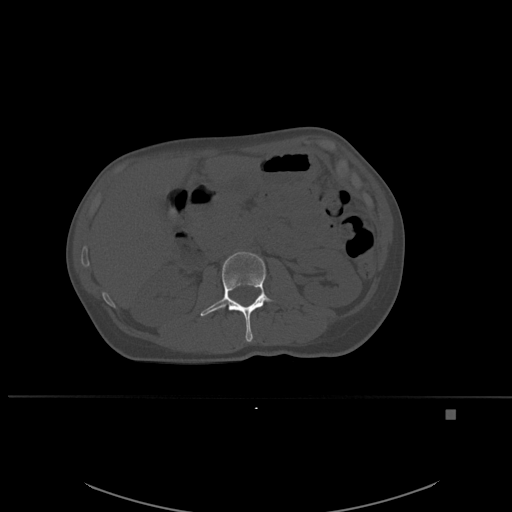
CT including the spine, one axial slice. Position 236 of 537 along the scan axis. Bone window (W 1800 / L 400 HU). 512 × 512 image matrix, field of view 440 × 440 mm. Female patient, age 45 years. Case-level facts recorded for this patient, not image findings: primary cancer: lung.
Annotated regions visible in this slice (semi-automatically segmented with operator editing):
- L2 vertebra: box from (x=200, y=252) to (x=273, y=342) px